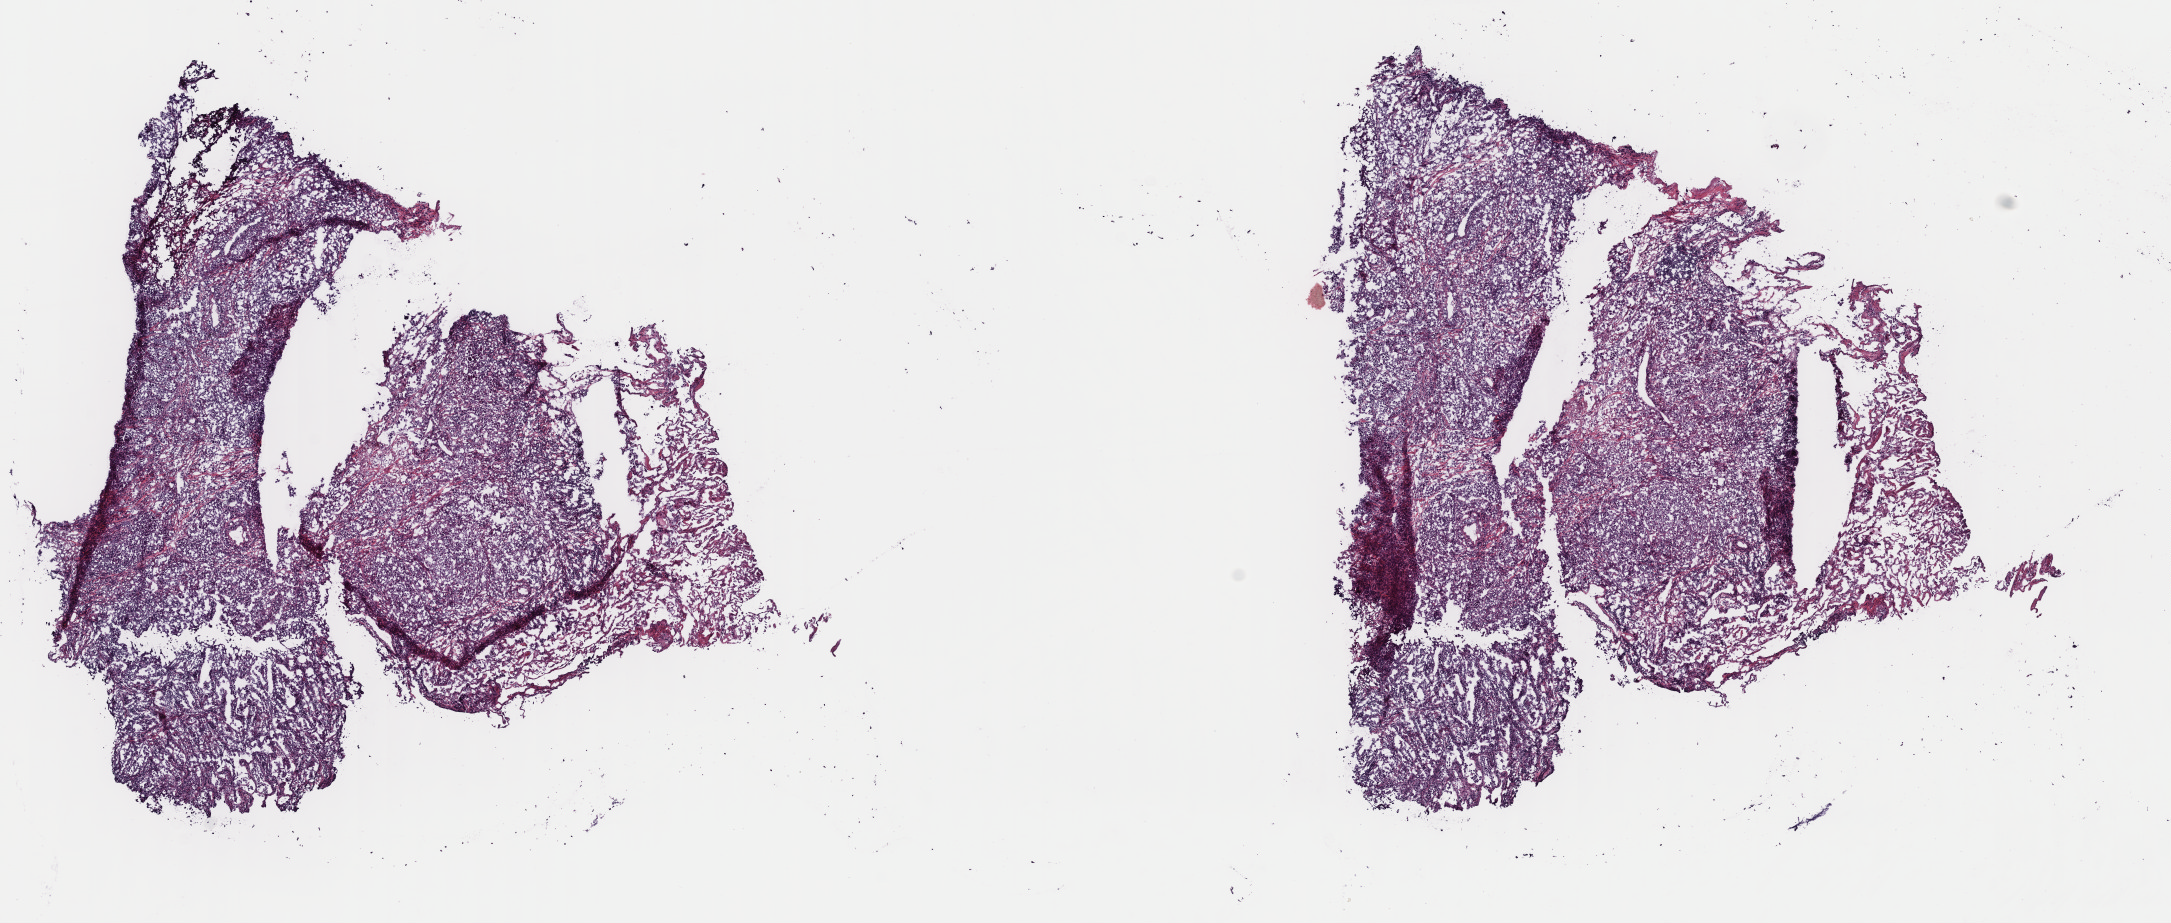
Digitized H&E-stained tissue section (whole slide), a low-resolution overview of the entire scanned area, about 17.1 x 7.3 mm; frozen section from the top of the tissue portion; primary tumour sample from the lung. Patient: female, age at initial diagnosis 69 years. Composition of this section per pathologist review: tumour cells 100%, tumour nuclei 65%, normal cells 0%, stromal cells 0%, necrosis 0%. Inflammatory infiltration, as recorded: lymphocyte infiltration 13%, monocyte infiltration 2%, neutrophil infiltration 0%.
• pathologic diagnosis: Adenocarcinoma with mixed subtypes (upper lobe, lung)
• AJCC pathologic stage: IA (7th edition)
• TNM: T1b N0 M0